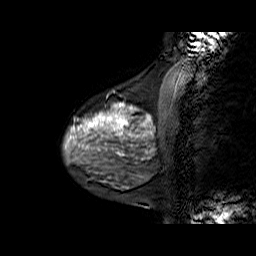
Breast MRI (dynamic contrast-enhanced), one sagittal slice; position 19 of 60 along the scan axis; dynamic contrast-enhanced series, time point 2 of 6 at this slice position (early post-contrast); 1.5 T; TE 6.3 ms, TR 32.9 ms; 256 × 256 image matrix, field of view 200 × 200 mm. Female patient. From the clinical record (not read from this slice): setting: breast cancer imaged before/during neoadjuvant chemotherapy; receptor status: HR-positive, HER2-negative.
Structures marked on this image (semi-automatic segmentation, software-assisted and operator-edited):
- analysis volume of interest (the breast-tissue region the enhancement analysis was run in; not a lesion): bounding box <65,86,169,170> (left, top, right, bottom; pixels)
- tumour enhancement mask (voxels above the 100 % enhancement threshold inside the analysis volume of interest): <70,102,153,155>